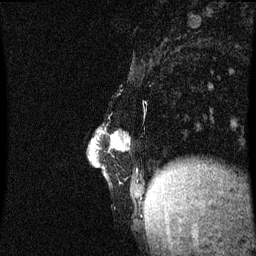
Breast MRI (dynamic contrast-enhanced), one sagittal slice. Position 14 of 60 along the scan axis. Dynamic contrast-enhanced series, image 2 of 3 at this slice position (ordered by acquisition). 1.5 T. TE 4.2 ms, TR 8.9 ms. 2 mm slice thickness. 256 × 256 image matrix. Patient: female, 47 years. Case-level facts recorded for this patient, not image findings: setting: breast cancer imaged before/during neoadjuvant chemotherapy; receptor status: HR-positive, HER2-negative.
Annotated regions visible in this slice (semi-automatic segmentation, software-assisted and operator-edited):
- analysis volume of interest (the breast-tissue region the enhancement analysis was run in; not a lesion): box from (x=91, y=130) to (x=147, y=197) px
- tumour enhancement mask (voxels above the 70 % enhancement threshold inside the analysis volume of interest): (x=115, y=136)–(x=122, y=147)